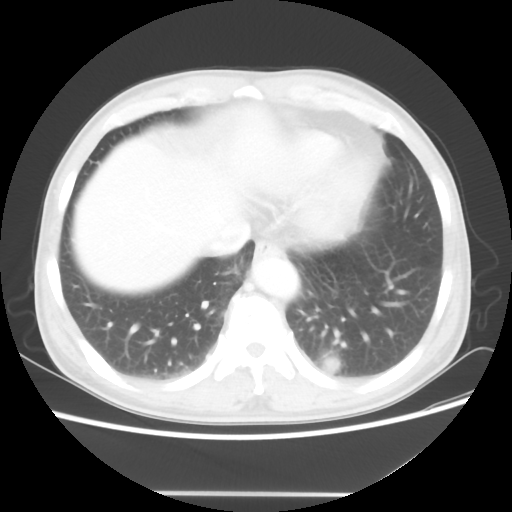
Chest CT, one axial slice. Position 16 of 60 along the scan axis. Lung window (W 1500 / L -600 HU). 5 mm slice thickness. 512 × 512 image matrix, field of view 360 × 360 mm. Male patient, age 55 years. From the clinical record (not read from this slice): clinical TNM (as recorded): T1c N3 M0.
Outlined on this slice (rectangle marked by the reading radiologist):
- lung tumour (recorded histology: small cell carcinoma): box from (x=318, y=353) to (x=345, y=379) px